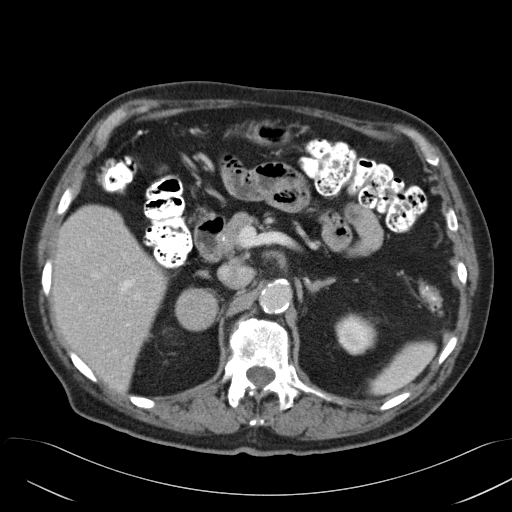
Contrast-enhanced abdominal CT, one axial slice. Slice 30 of 58 in the series (ordered by position). Reconstruction kernel B31f. 120 kVp. Intravenous contrast given. Soft-tissue window (W 400 / L 40 HU). 5 mm slice thickness. 512 × 512 image matrix, field of view 384 × 384 mm. Male patient, age 82 years. From the clinical record (not read from this slice): diagnosis: adrenocortical carcinoma; tumour side: right adrenal; tumour size at pathology: 9 cm; Ki-67 index: 30 %; stage (as recorded): 3.
Structures marked on this image (semi-automatically segmented with operator editing):
- mass: box from (x=184, y=291) to (x=213, y=325) px